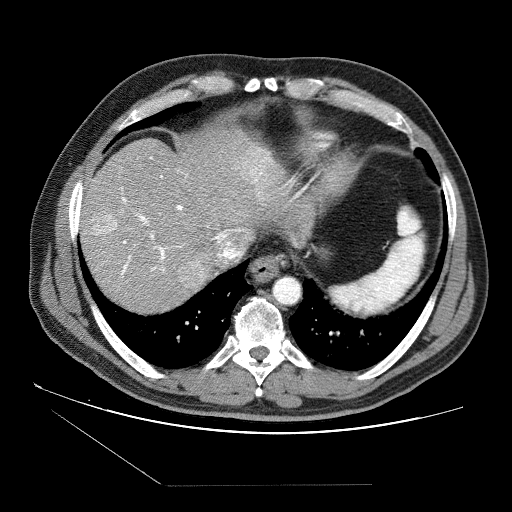
Contrast-enhanced abdominal CT (liver protocol), one axial slice. Slice 70 of 87 in the series (ordered by position). 120 kVp. Soft-tissue window (W 400 / L 40 HU). 2.5 mm slice thickness. 512 × 512 image matrix. Case-level facts recorded for this patient, not image findings: diagnosis: hepatocellular carcinoma (patient treated with transarterial chemoembolisation; whether this scan precedes or follows treatment is not stated here); TNM stage (as recorded): Stage-II.
Outlined on this slice (semi-automatically segmented with operator editing):
- abdominal aorta: bounding box <273,276,300,303> (left, top, right, bottom; pixels)
- liver parenchyma outside the tumour (the mass and vessels are separate outlines, so this box may not span the whole liver): <80,128,290,312>
- mass: <93,147,273,289>
- liver vessels: <90,156,244,277>